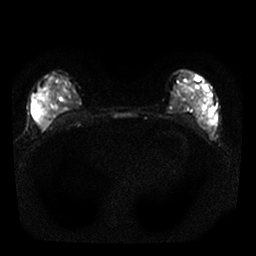
Breast MRI, one axial slice; slice 14 of 25 in the series (ordered by position); diffusion-weighted series; image 2 of 4 stored at this slice position (different b-values; order by instance number); 1.5 T; 4 mm slice thickness; 256 × 256 image matrix, field of view 290 × 290 mm. Female patient.
Structures marked on this image (outlined manually by an expert reader):
- tumour on diffusion-weighted imaging: bounding box (x1, y1, x2, y2) in pixels: (38, 78, 71, 129)